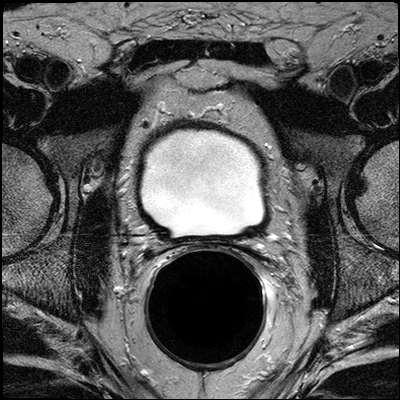
MRI of the prostatic bed after radical prostatectomy; 3 images, each a single mid-volume slice chosen by position (not for content). Treatment context recorded for this patient: Surgery.
Image 1: axial T2-weighted image, slice 17 of 32.
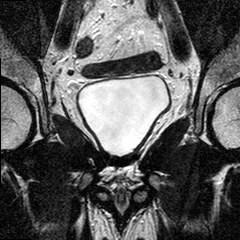
Image 2: coronal T2-weighted image, series "T2W_TSE_COR", slice 13 of 24.
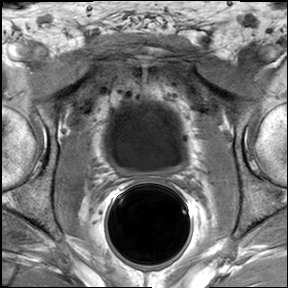
Image 3: DCE (dynamic gadolinium-enhanced) axial slice, series "AX BLISS_GAD_8", slice 18 of 34, dynamic phase 2 of 2, 6 mm slice thickness.
Radiologist's MRI report for this examination:
Indication: Patient is status post radical prostatectomy. Now with rising PSA. Pre planning examination.
FINDINGS:
Regular findings seen within the surgical bed. Multiple surgical clips within the prostatic bed and around the anastomosis. Regular appearance of the anastomosis. No definite masses seen within the prostatic bed. No foci of suspicious enhancement in and around the prostatic bed. Unremarkable urinary bladder. No remnant seminal vesicles present. No suspiciously enlarged obturator and iliac lymph nodes. The visualized osseous structures without evidence of involvement.
IMPRESSION: Expected post surgical appearance of the prostatic bed and anastomosis. No suspicious mass in the surgical bed. No enlarged obturator or iliac lymph nodes.

Prostatectomy specimen pathology (as recorded; the prostatectomy preceded this MRI, which images the post-surgical bed):
The specimen consists of a prostatectomy specimen with attached left and right seminal vesicles and attached segments of the vas deferens. The specimen weighs 33.5gms and measures 8x4.1x3.8 cm in greatest dimension. The right and left seminal vesicles measure 3.8x2.6x0.8 cm and 3.1x1.9x0.9 cm, respectively. The left vas deferens measures 4.5 cm in length and 0.5 cm in diameter. The right vas deferens measures 4.5 cm in length and 0.4 cm in diameter. The prostate is symmetrical and firm. The right side is inked black and he left side is inked blue. Sectioning reveals no grossly identifiable tumors. The prostatic parenchyma is gray/white and nodular in appearance. Representative sections are submitted in cassettes as follows: 1 distal urethral margin, 2 bladder neck margin, 3 left and right vas deferens margins, 4 left seminal vesicle margin, 5 right seminal vesicle margin, 6 thru 10 left anterior lobe sectioned from apex to base, 11 thru 15 left posterior lobe sectioned from apex to base, 16 thru 19 right anterior lobe sectioned from apex to base, 20 thru 22 right posterior lobe sectioned from apex to base. Specimen(s) Received PROSTATE GLAND
PROSTATIC ADENOCARCINOMA, CONVENTIONAL-TYPE. GLEASON GRADE 3+4 SCORE = 7/10. THE TUMOR IS CONFINED TO THE PROSTATE GLAND AND IS BILATERAL. THE TUMOR OCCUPIES 10% OF THE TOTAL GLAND. INVASION OF SEMINAL VESICLES IS NOT IDENTIFIED. PERINEURAL INVASION IS PRESENT. LYMPHOVASCULAR SPACE IS ABSENT. THE SURGICAL MARGINS ARE POSITIVE, (LEFT APICAL AND RIGHT MID POSTERIOR). ADDITIONAL PATHOLOGIC FINDINGS: HIGH GRADE PROSTATIC INTRAEPITHELIAL NEOPLASIA, CHRONIC INFLAMMATION. AJCC PATHOLOGIC STAGE II (pt2c, pnx, pmx).